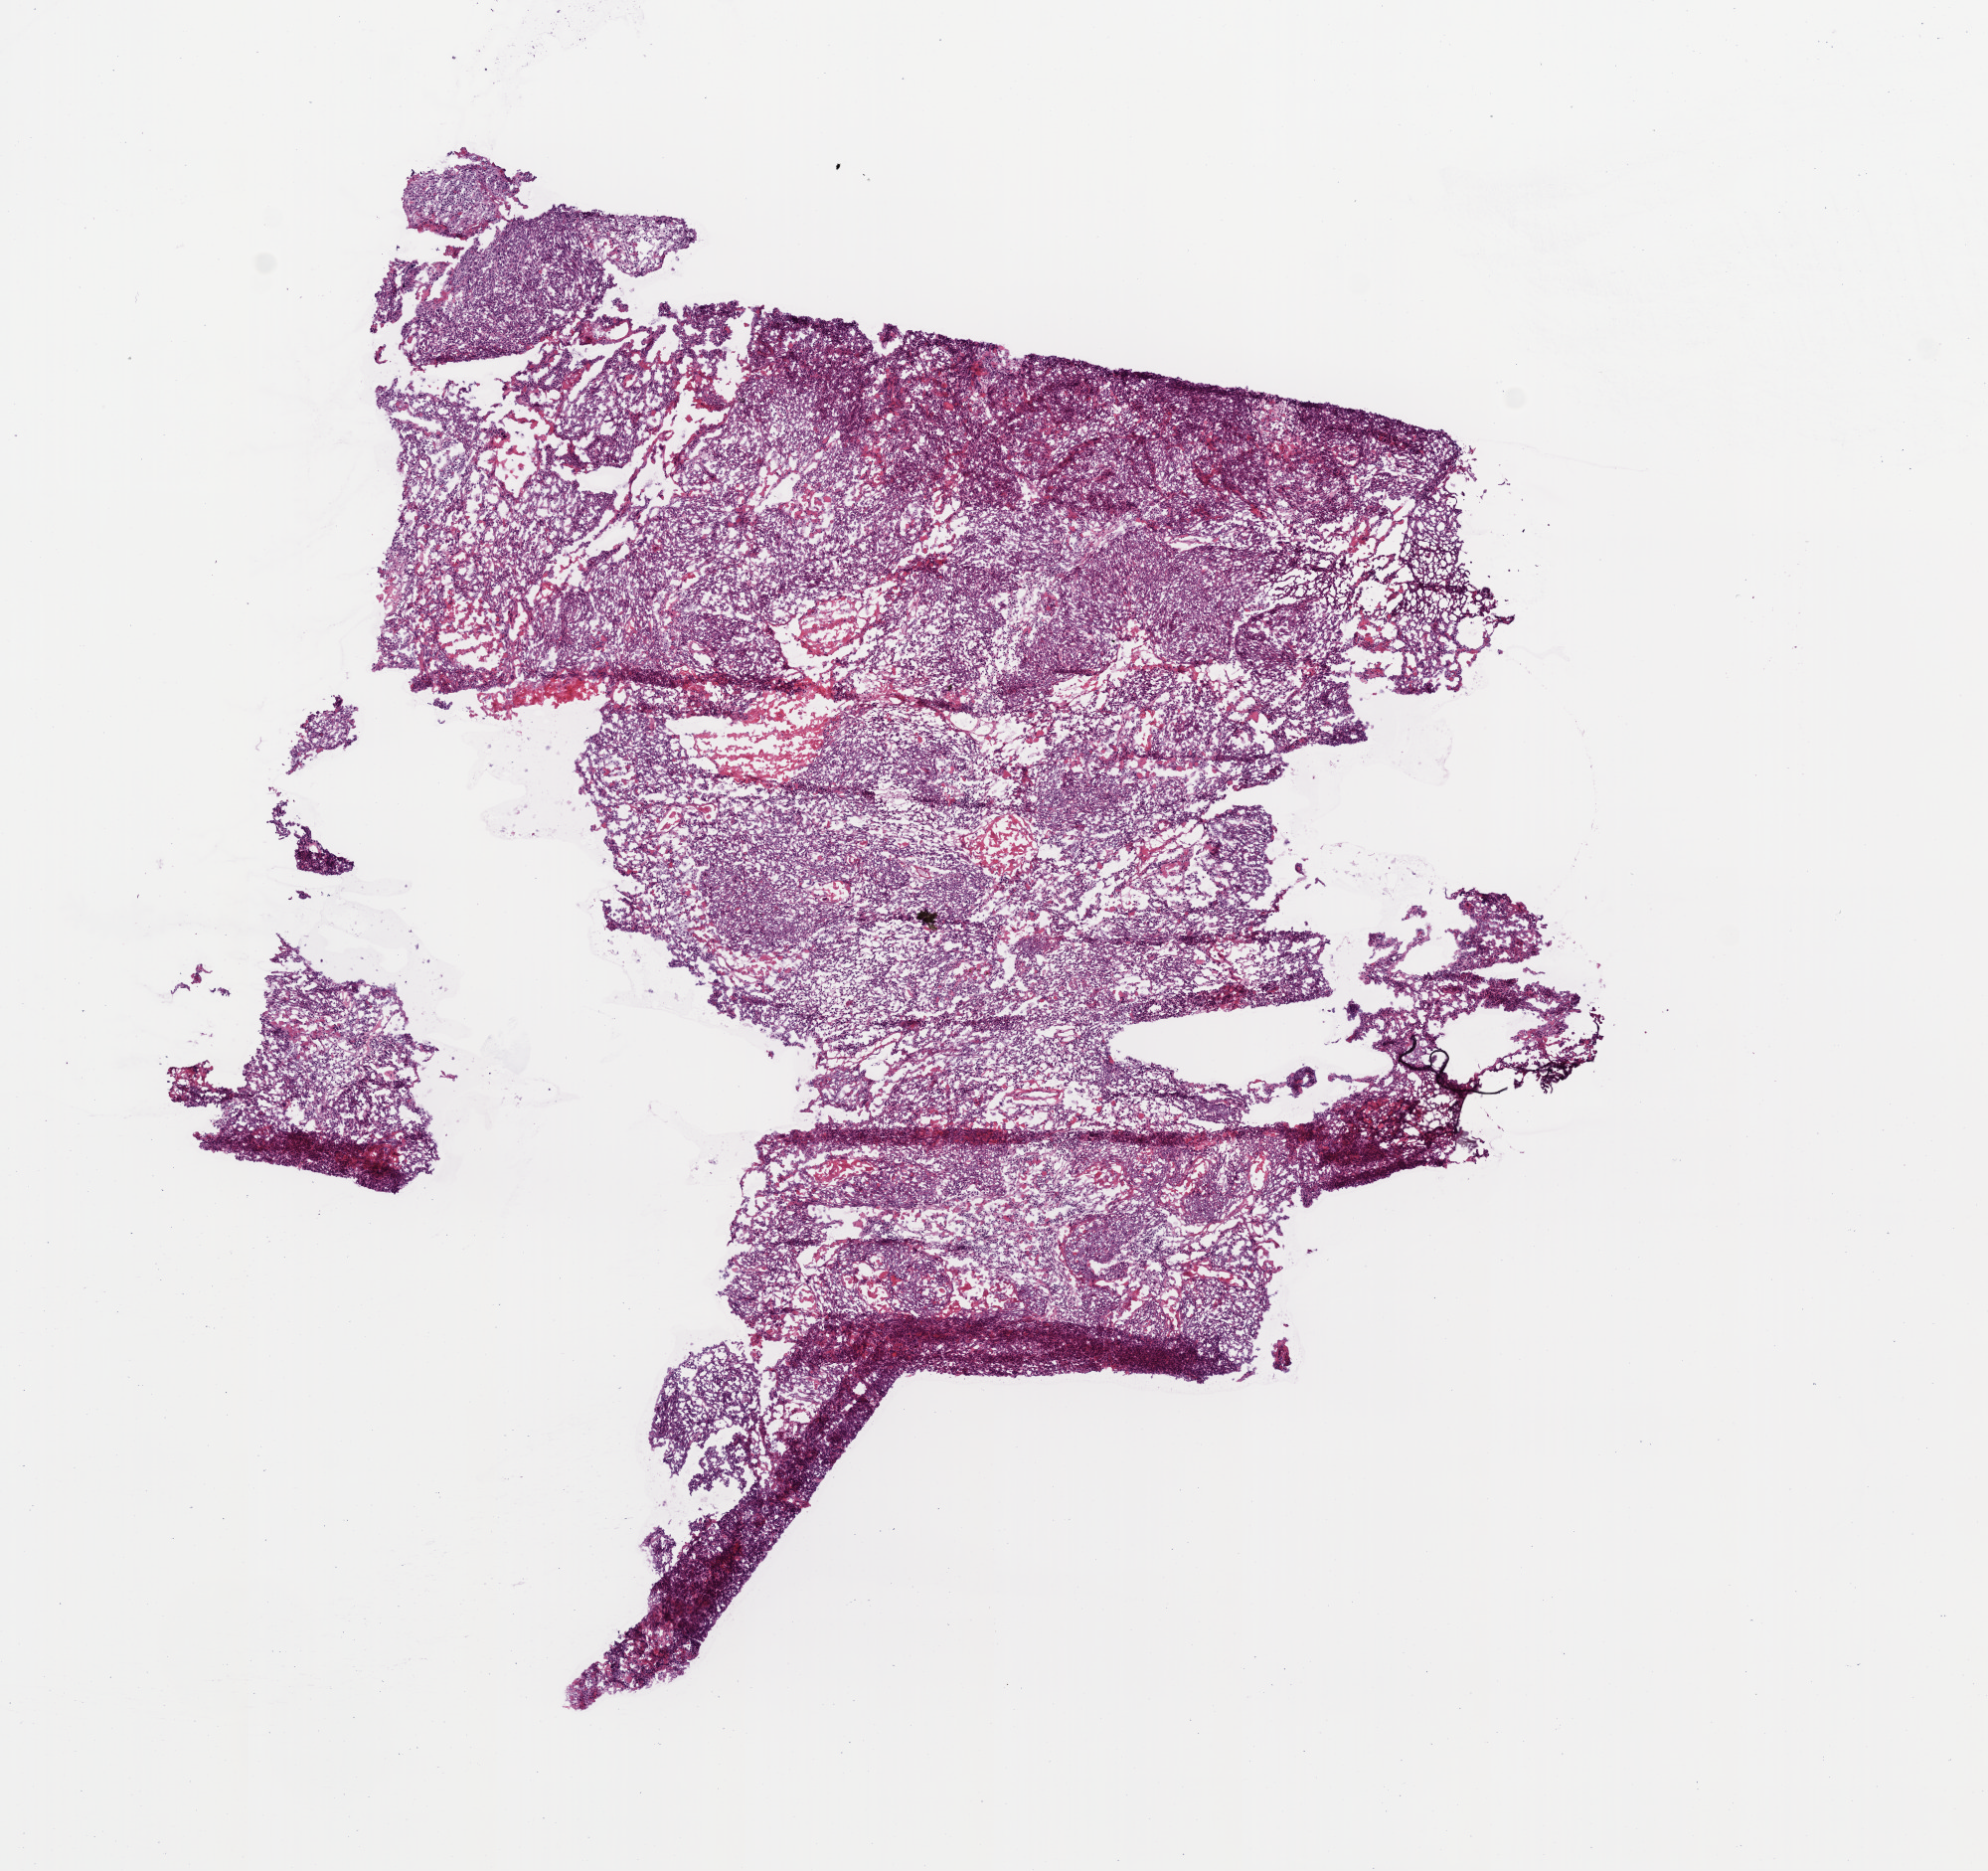
H&E-stained whole-slide image, a low-resolution overview of the entire scanned area, about 8.0 x 7.6 mm (slide scanned at 20x); frozen section from the bottom of the tissue portion; primary tumour sample from the head and neck. Patient: male, age at initial diagnosis 73 years. Histologic grade: G3 (poorly differentiated). Slide review estimates, as recorded: tumour cells 90%, tumour nuclei 92%, normal cells 0%, stromal cells 0%, necrosis 10%. Infiltration values recorded for this section: lymphocyte infiltration 5%.
• pathologic diagnosis: Squamous cell carcinoma, NOS (base of tongue, NOS)